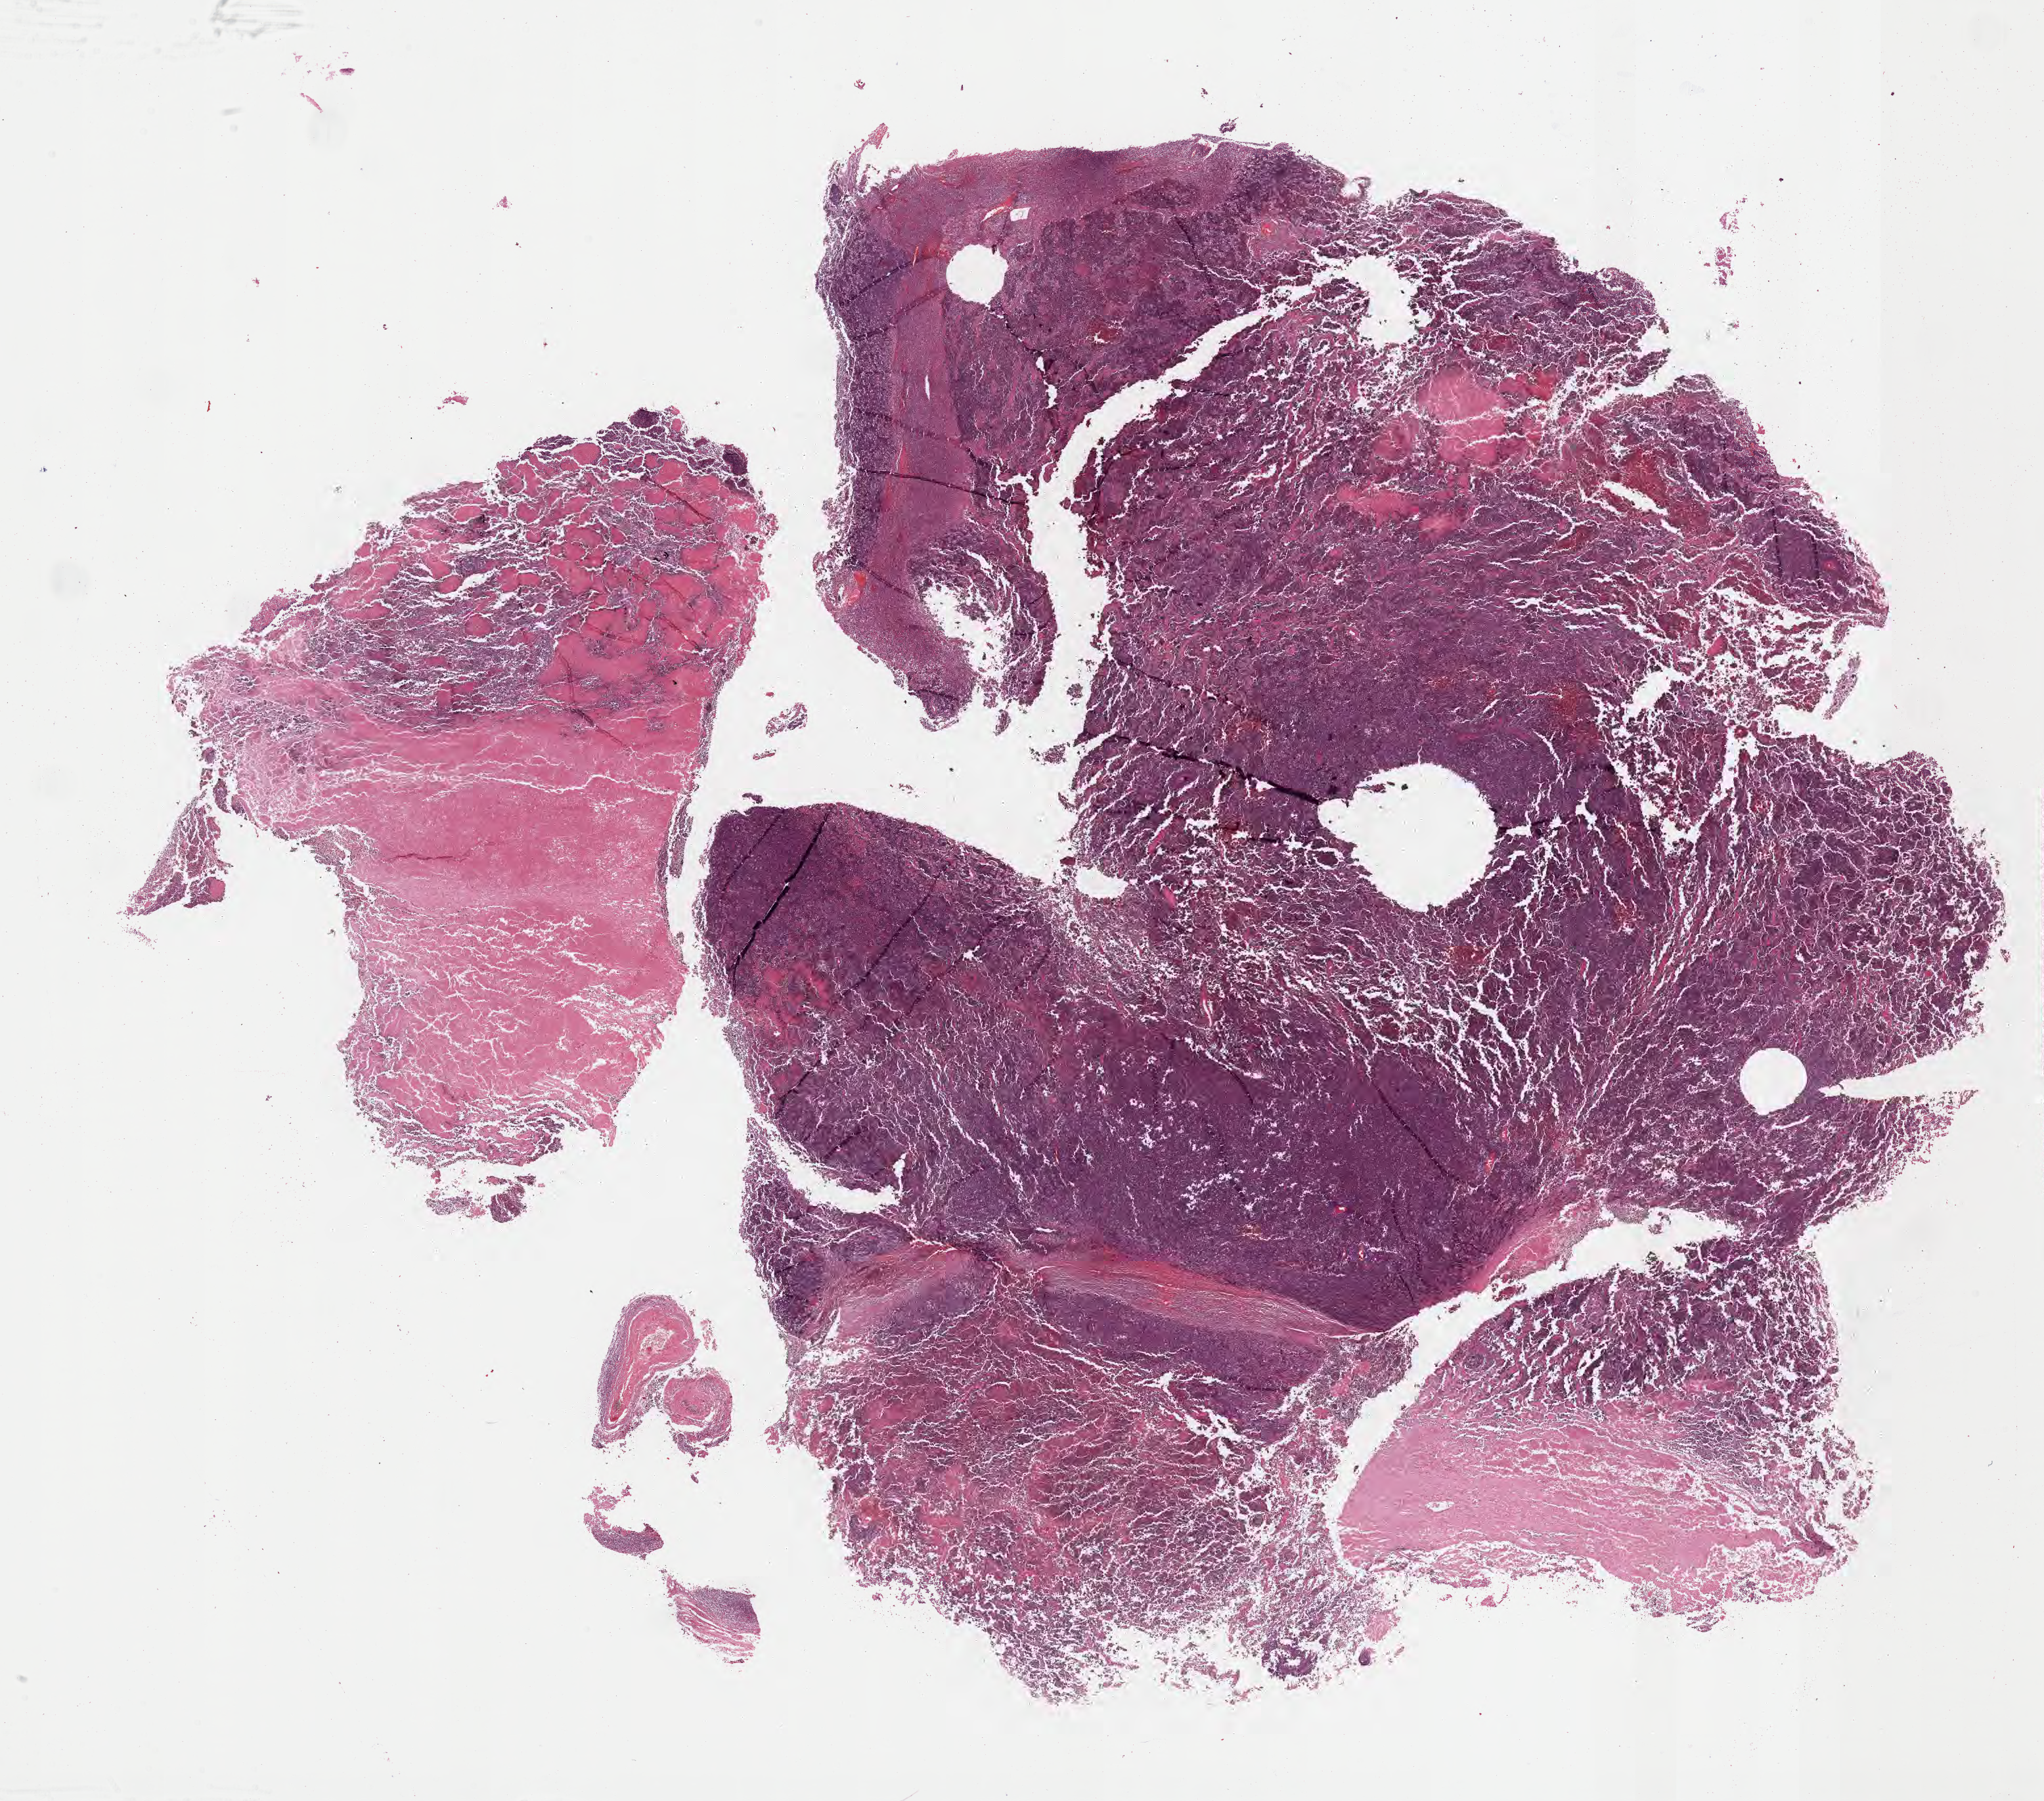
Digitized hematoxylin and eosin (H&E)-stained section — whole scanned area (about 25.2 x 22.2 mm) shown as a low-resolution overview; formalin-fixed paraffin-embedded section; primary tumor. Female patient, aged 34. Pathologist review of this section (percent, as recorded): tumor cells 60%, tumor nuclei 90%, stromal cells 10%, necrosis 30%, normal cells 0%. Inflammatory infiltration, as recorded: lymphocyte infiltration 50%, monocyte infiltration 20%, neutrophil infiltration 10%.
Ann Arbor stage (patient): Stage IV. Histologic diagnosis: Burkitt lymphoma, NOS. Section: bottom of the tissue portion.